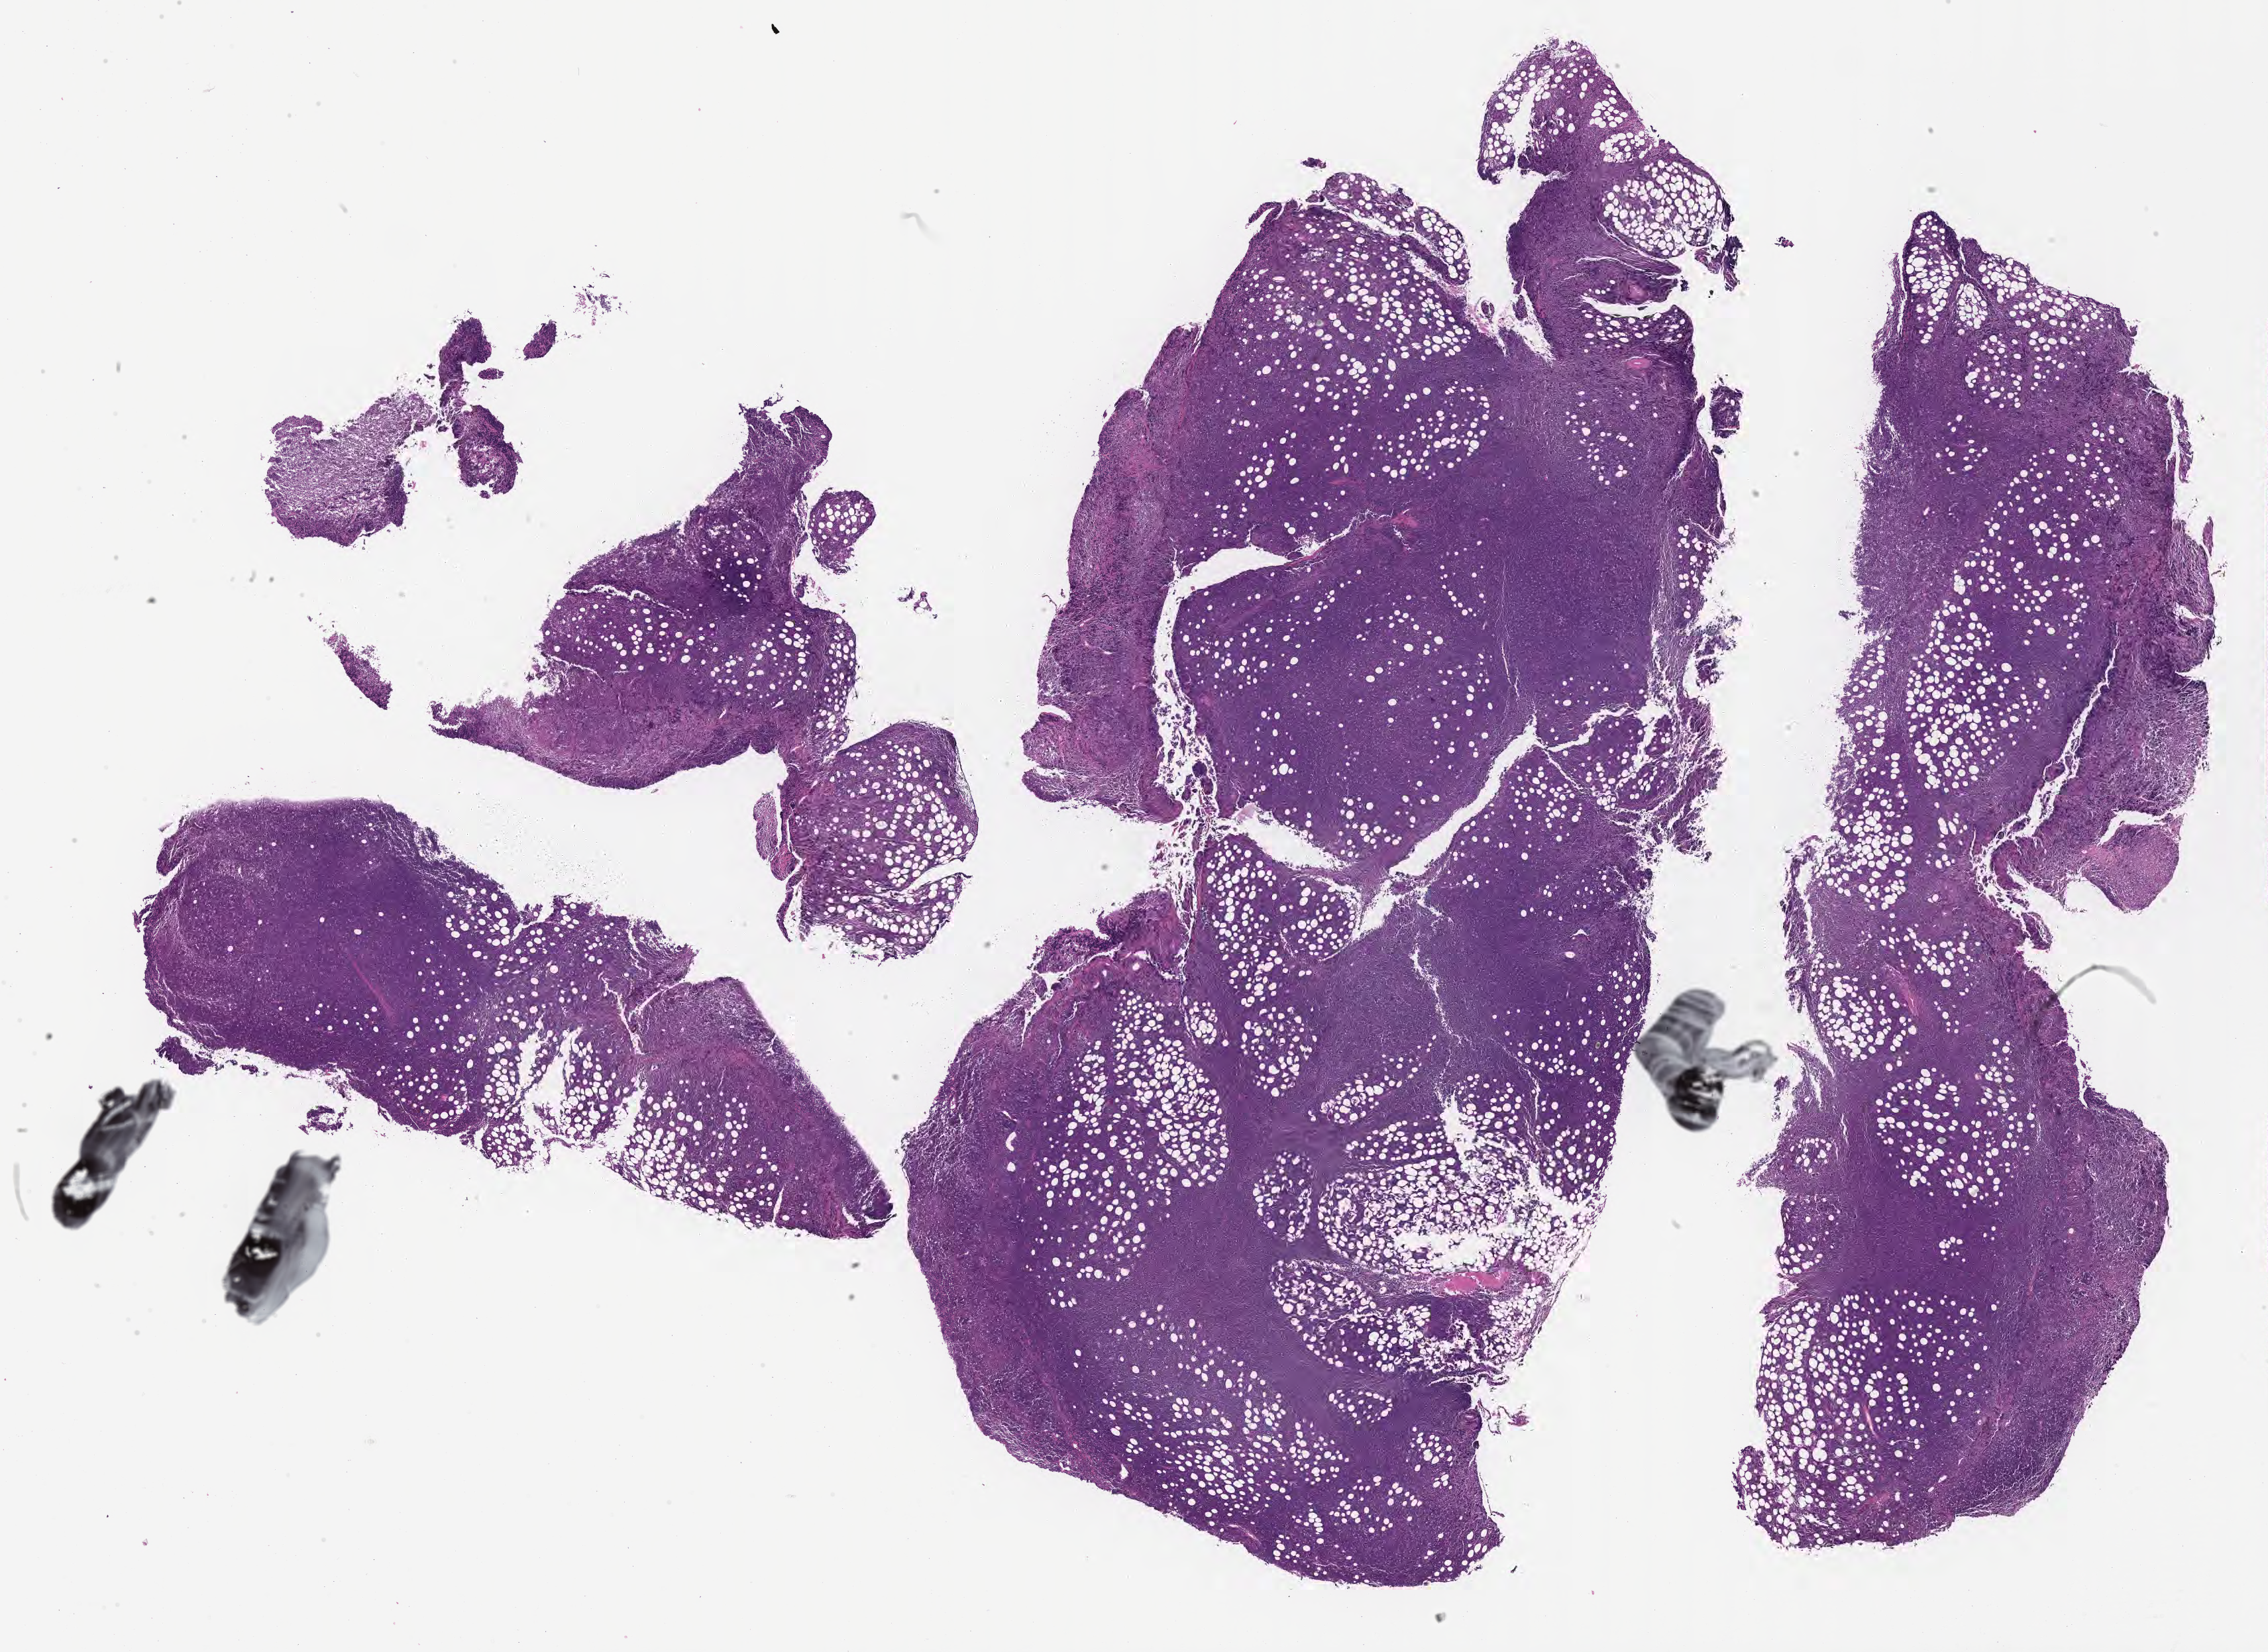
Whole-slide image, haematoxylin and eosin stain, a low-resolution overview of the entire scanned area, about 27.7 x 20.2 mm; specimen: tumor tissue. Patient male; 31 years old.
Histologic diagnosis: Burkitt lymphoma, NOS.